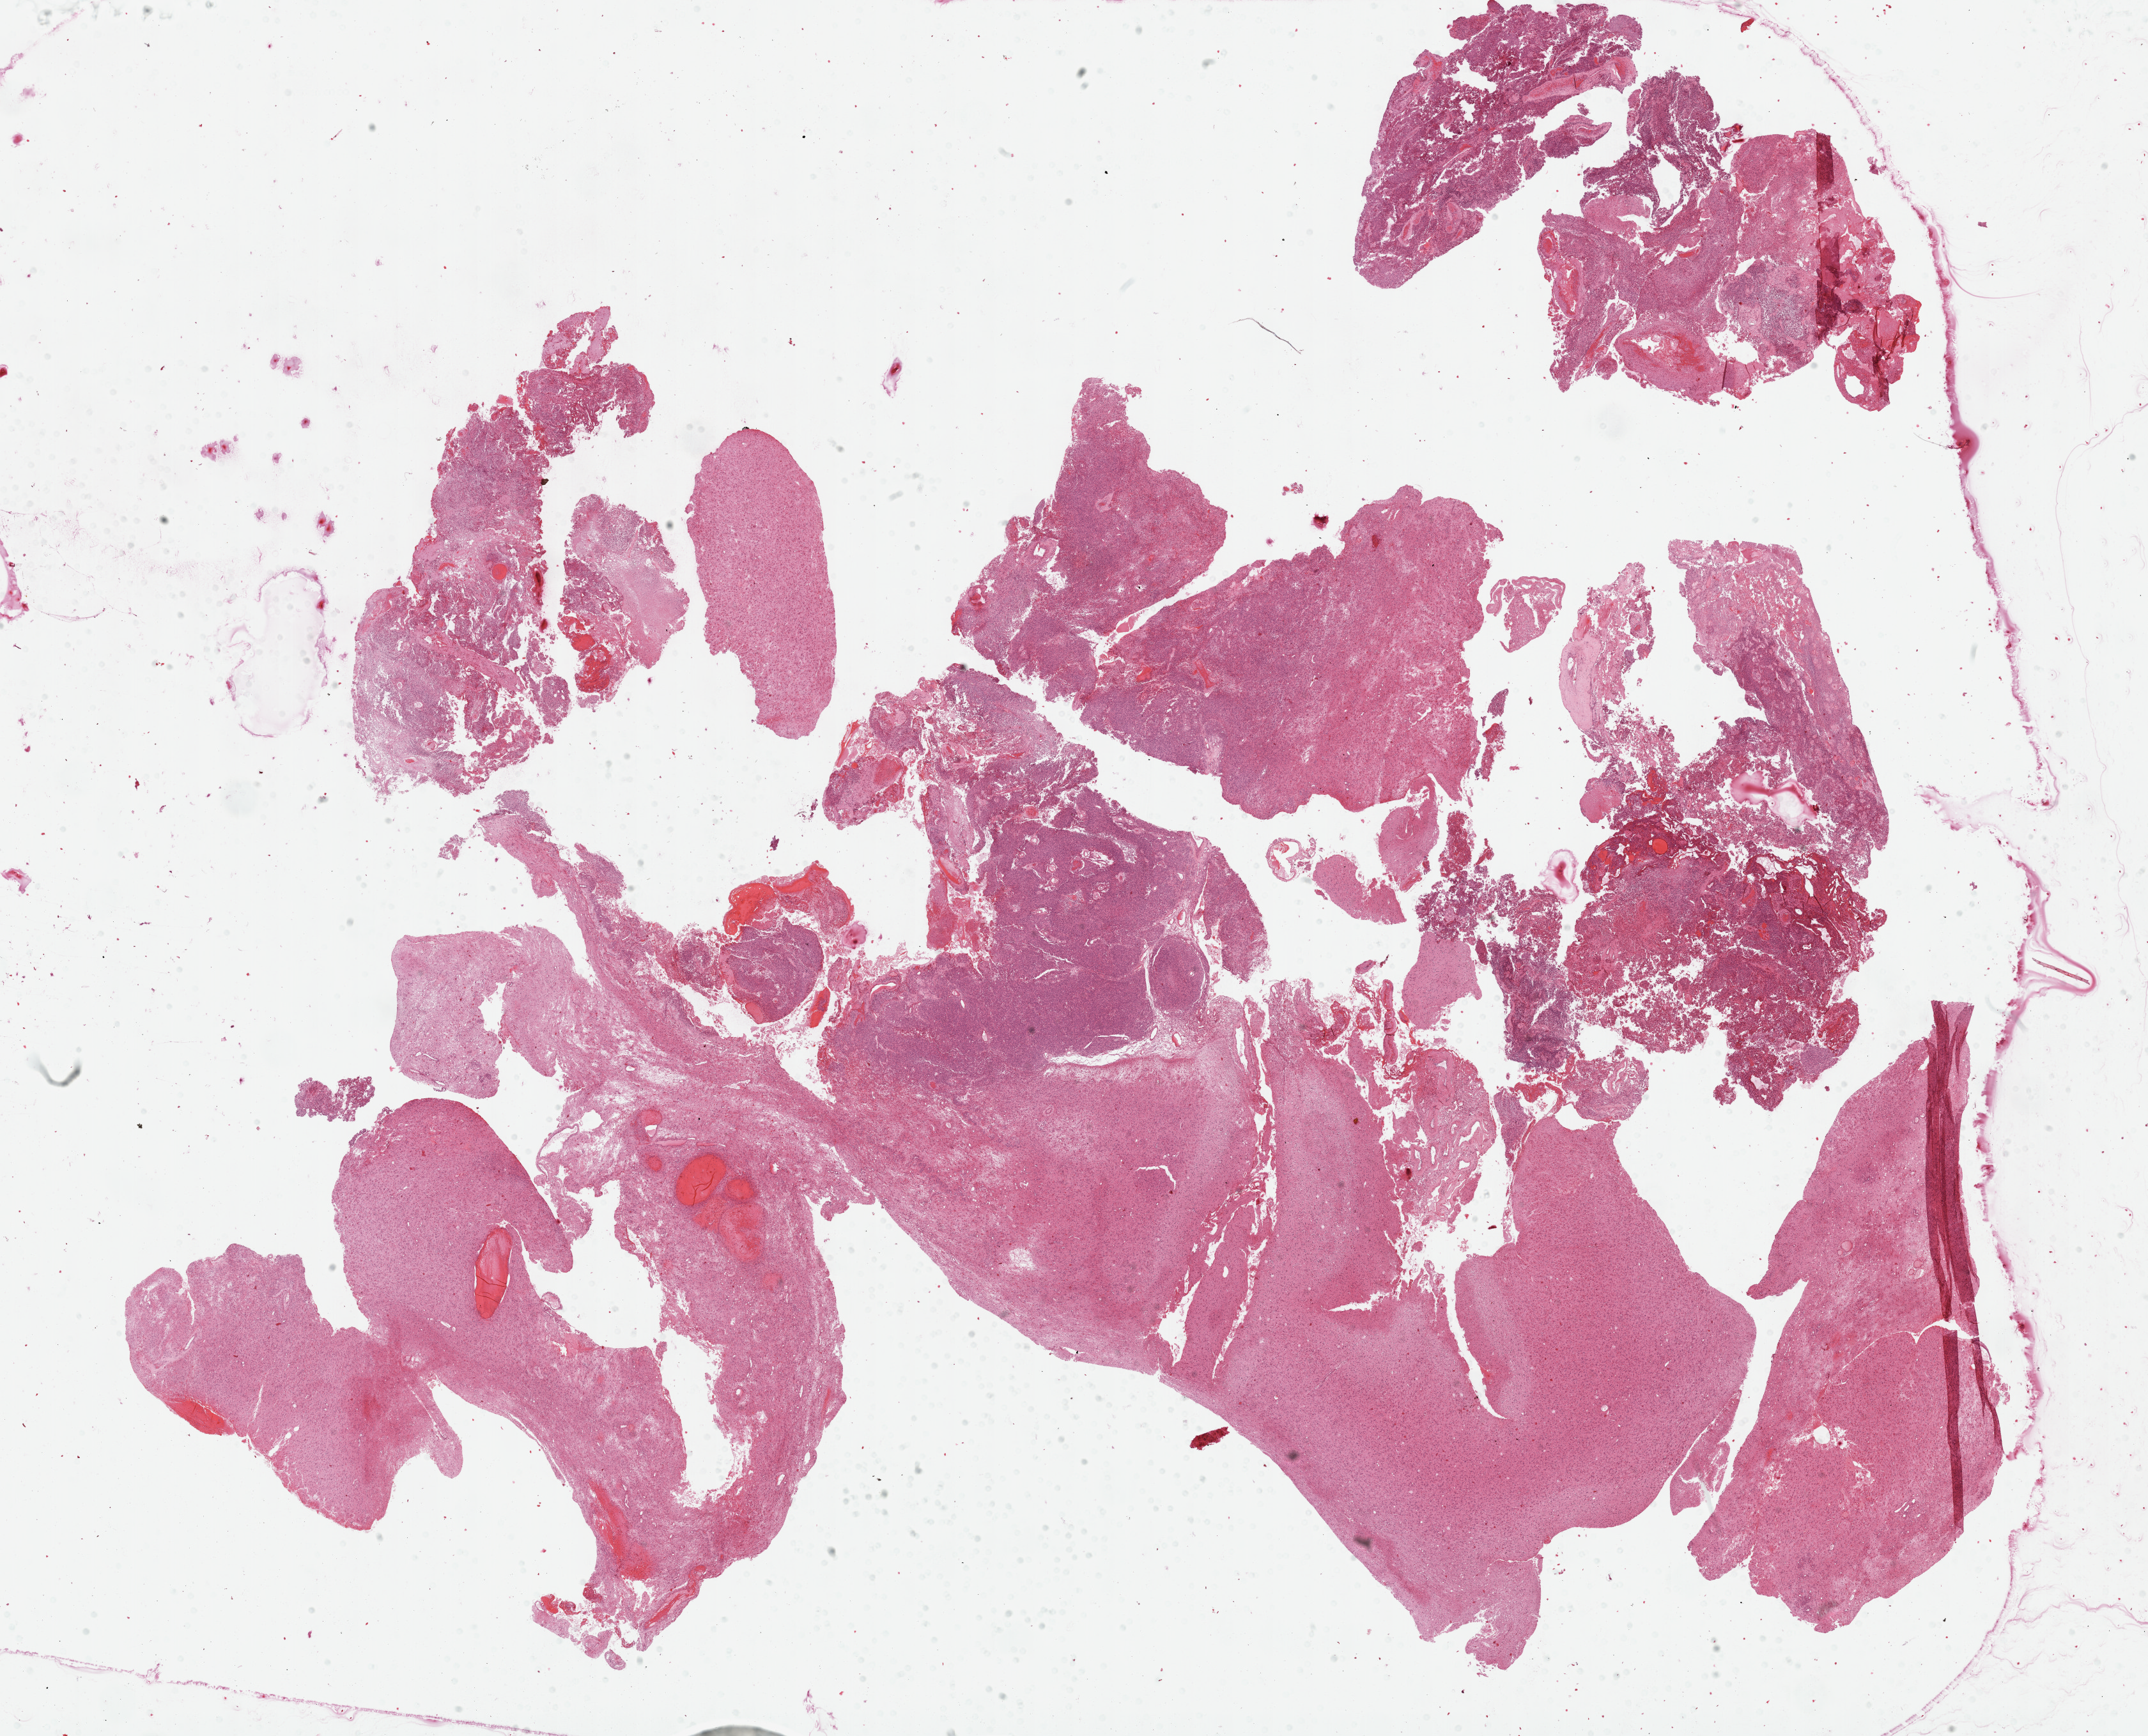
H&E whole-slide image — shown as a low-resolution overview of the whole scanned area (about 27.2 x 22.0 mm, acquisition: 40x scan), formalin-fixed paraffin-embedded (FFPE) diagnostic section, primary tumour sample from the brain. Male, age 52 years at initial diagnosis.
Diagnosis: Glioblastoma.